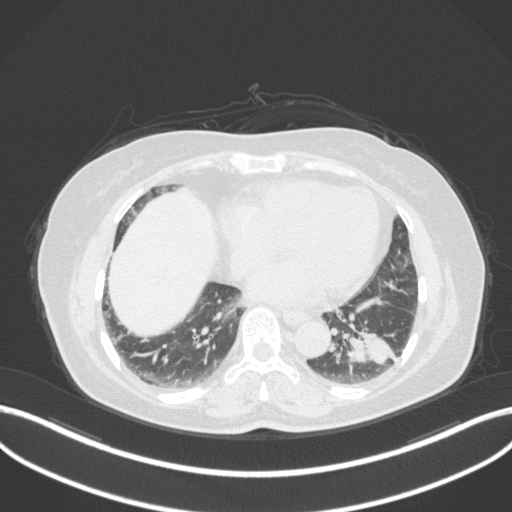
Chest CT, one axial slice; 120 kVp; lung window (W 1500 / L -600 HU); 512 × 512 image matrix, field of view 400 × 400 mm. Female patient, age 59 years. From the clinical record (not read from this slice): clinical TNM (as recorded): T2a N0 M0; histopathological grade: G2-3.
Annotated regions visible in this slice (rectangle marked by the reading radiologist):
- lung tumour (recorded histology: adenocarcinoma): bounding box (x1, y1, x2, y2) in pixels: (337, 322, 401, 374)